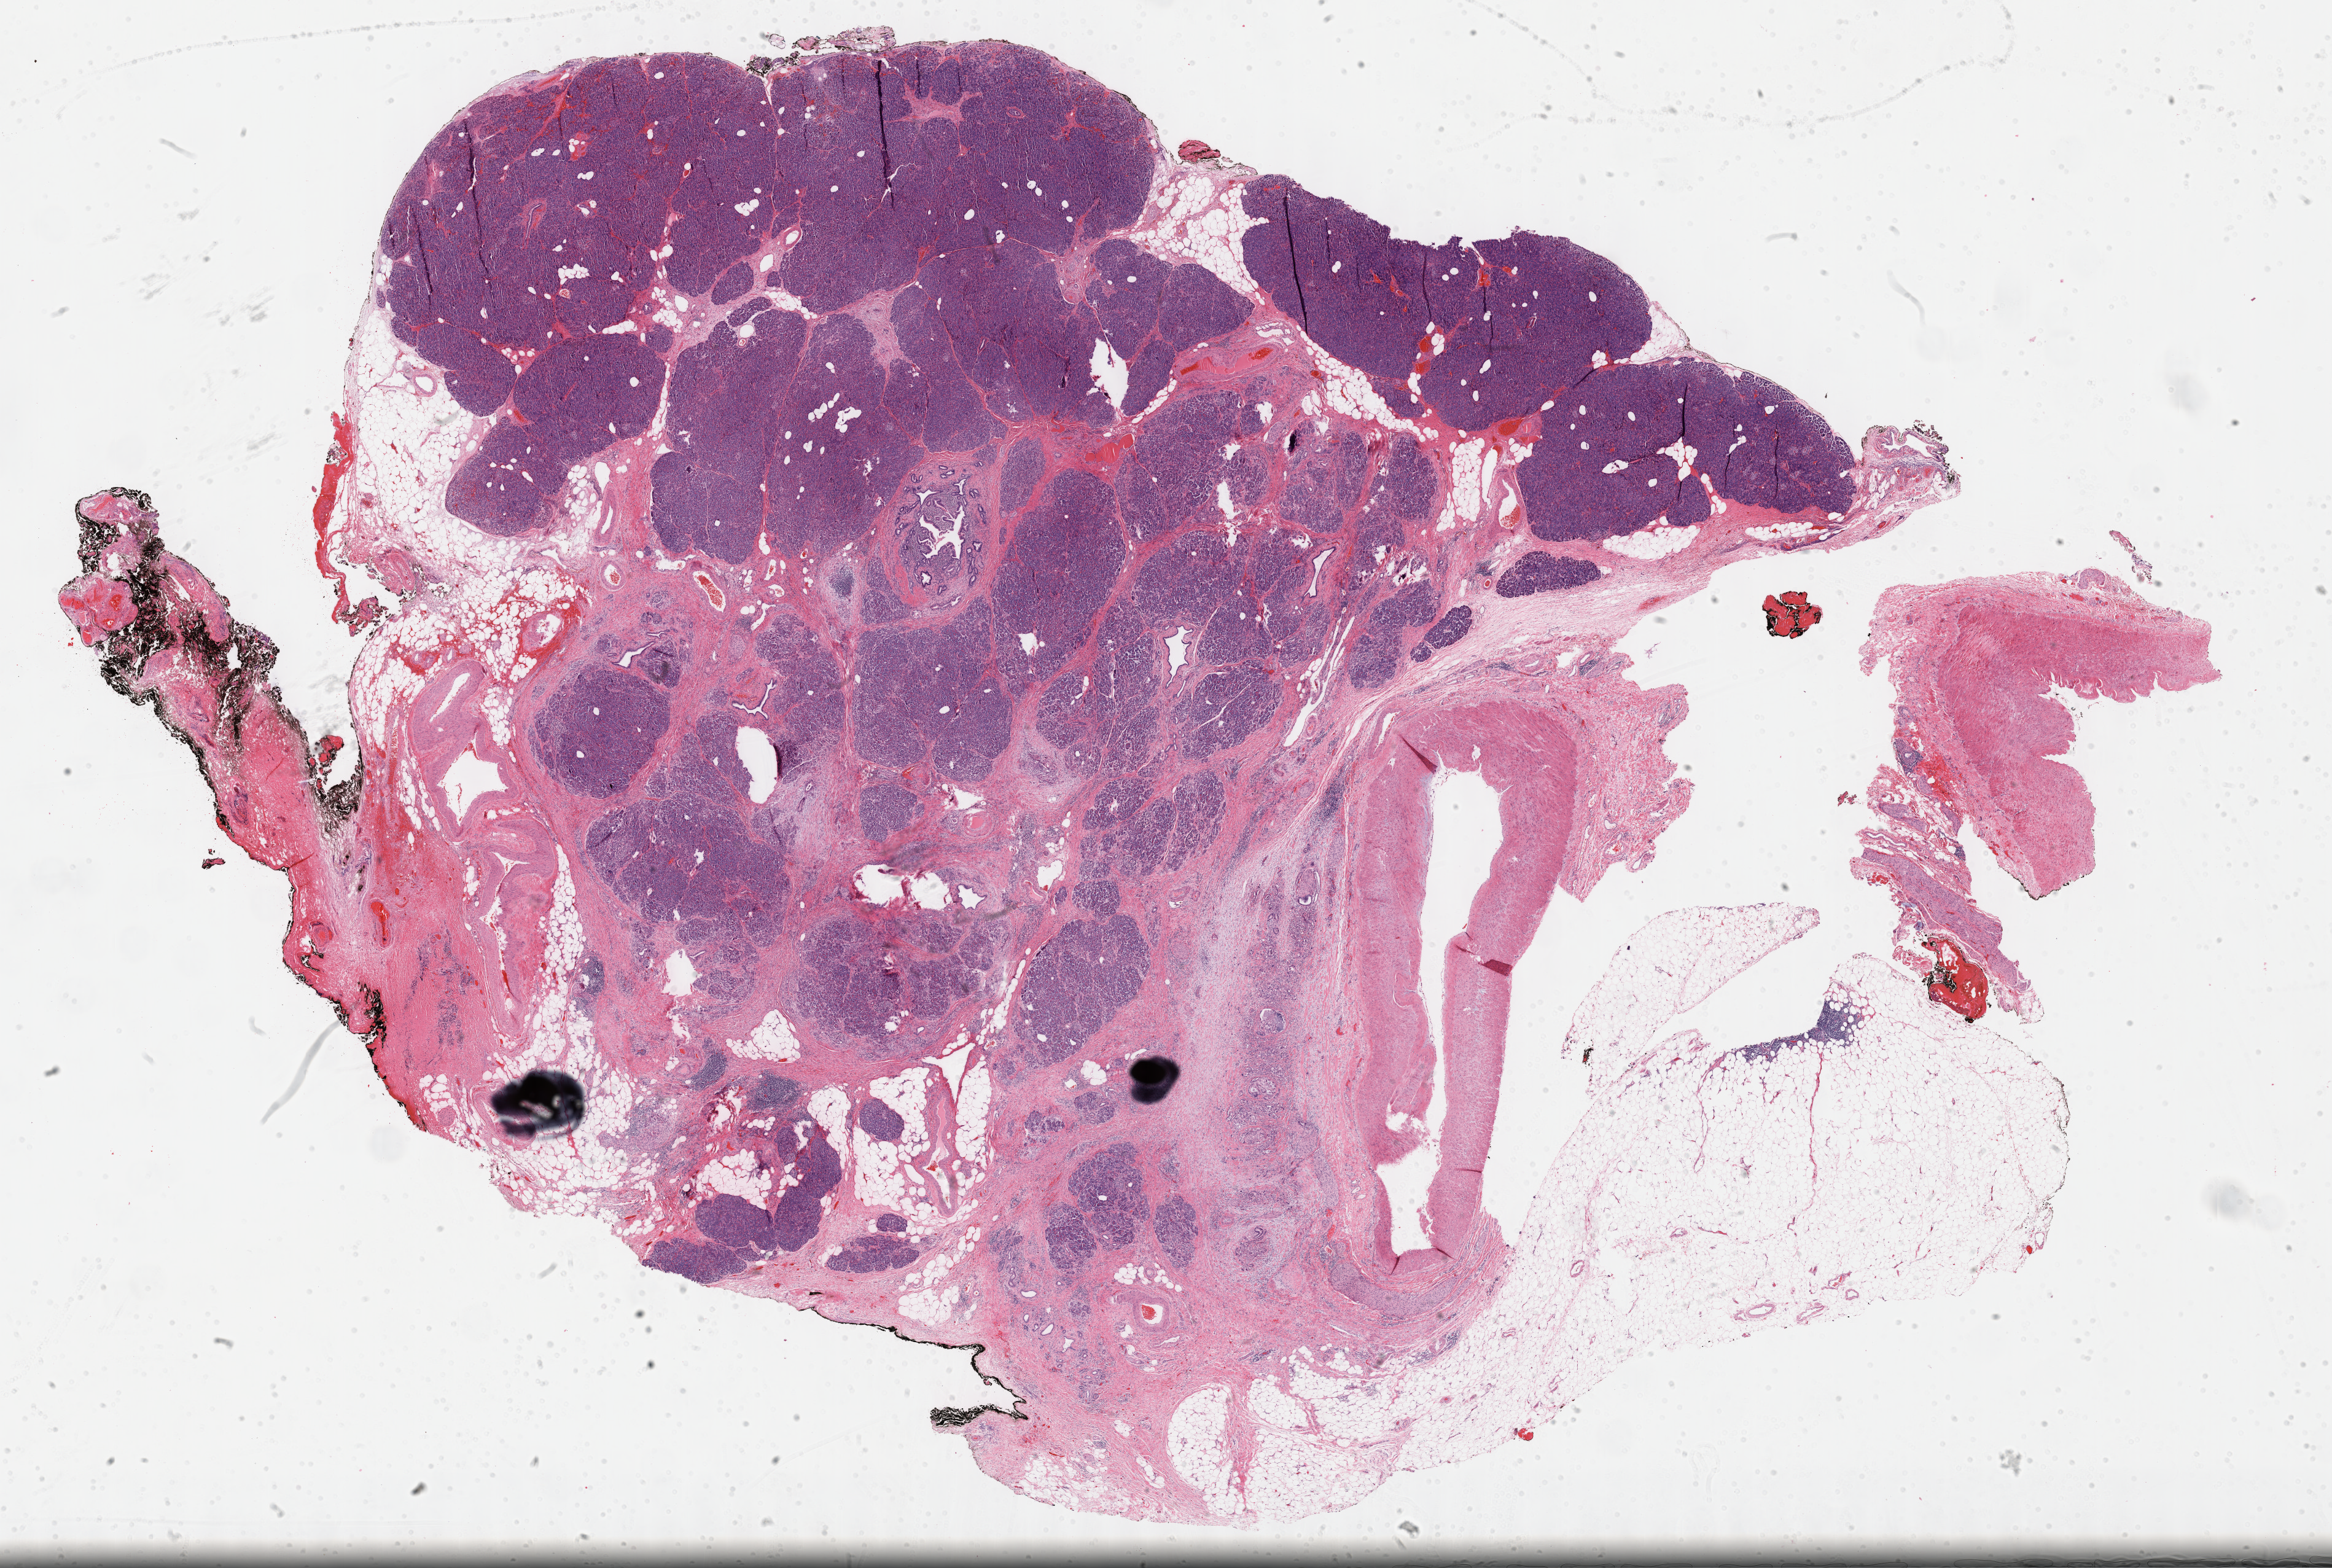
H&E whole-slide image, shown as a low-resolution overview of the whole scanned area (about 30.7 x 20.6 mm, acquisition: 40x scan), formalin-fixed paraffin-embedded (FFPE) diagnostic section, sample: primary tumour, pancreas. Female patient; age at initial diagnosis 66 years. Histologic grade: G2 (moderately differentiated).
* AJCC pathologic stage: IV (7th edition)
* TNM: T3 N1 M1
* histologic diagnosis: Infiltrating duct carcinoma, NOS (body of pancreas)
* lymph nodes positive (case pathology): 1 of 12 examined